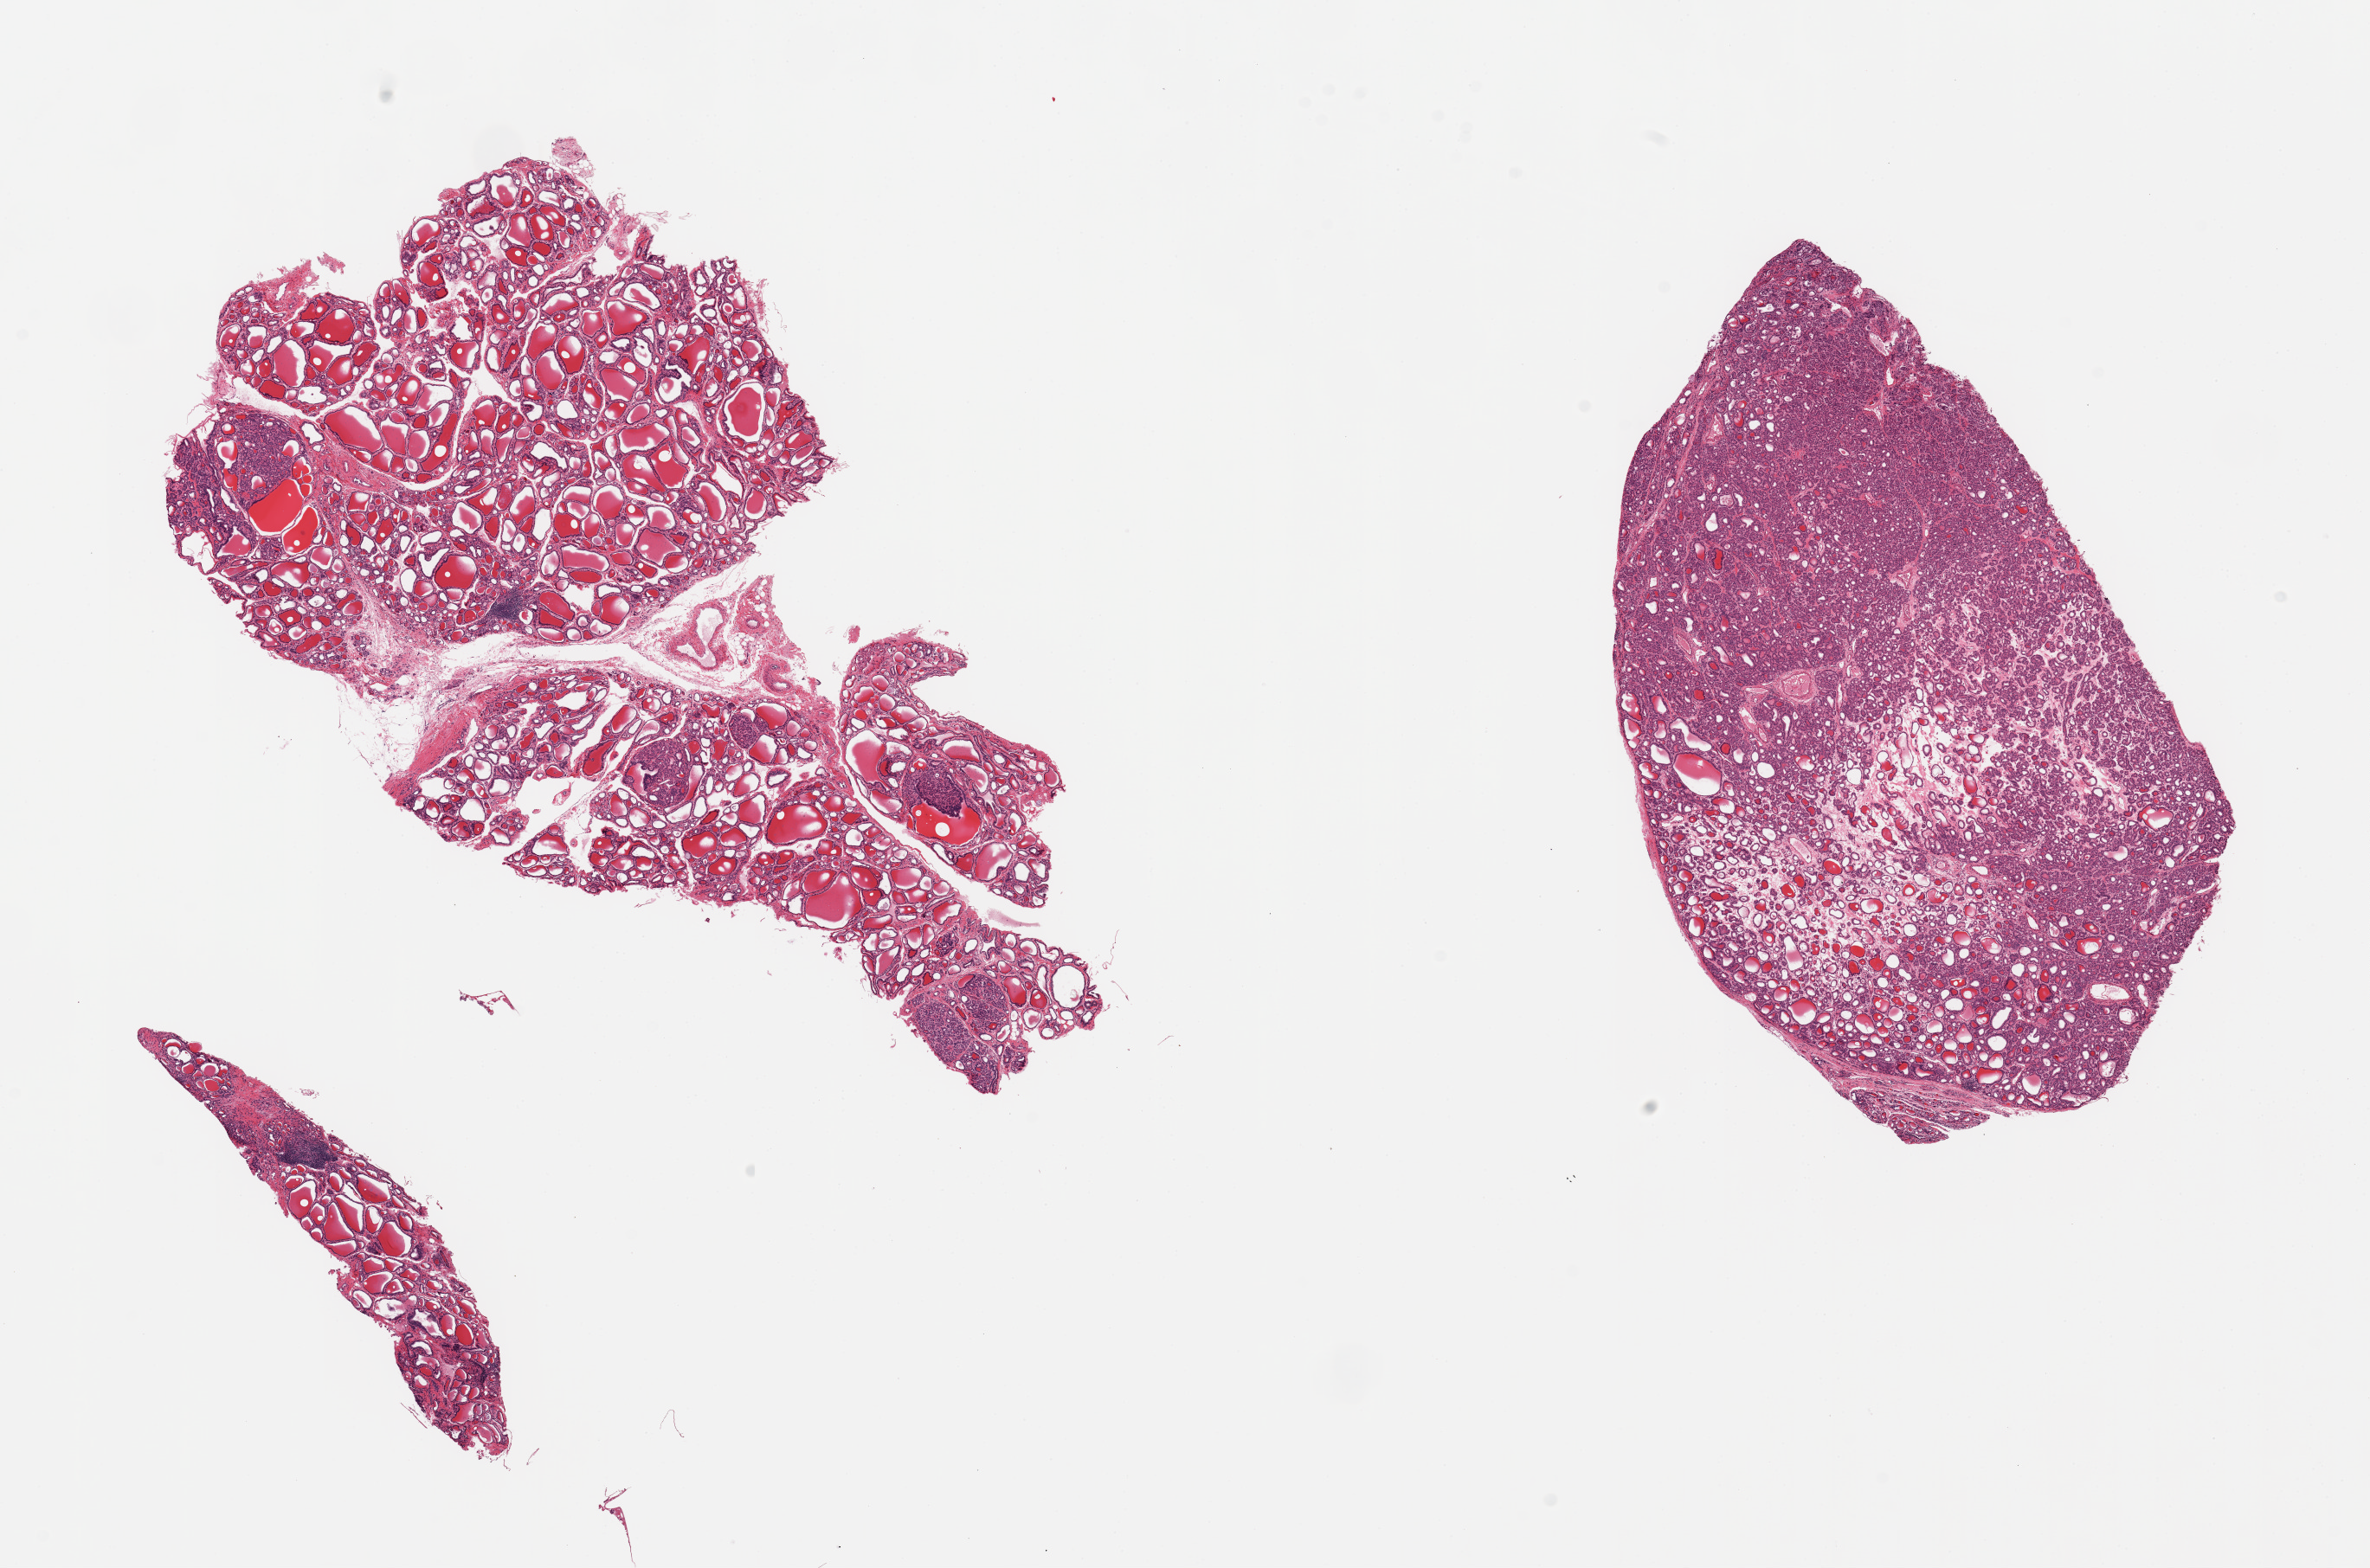
H&E whole-slide image, brightfield — a low-resolution overview of the entire scanned area, about 21.7 x 14.3 mm (slide scanned at 20x), PAXgene-fixed, paraffin-embedded tissue, target tissue: thyroid, tissue donor sample. Donor sex: female.
- pathologist's review note for this sample: 2 pieces, noudular (microfollicular) goiter, focal lymphyocytic thyroiditis